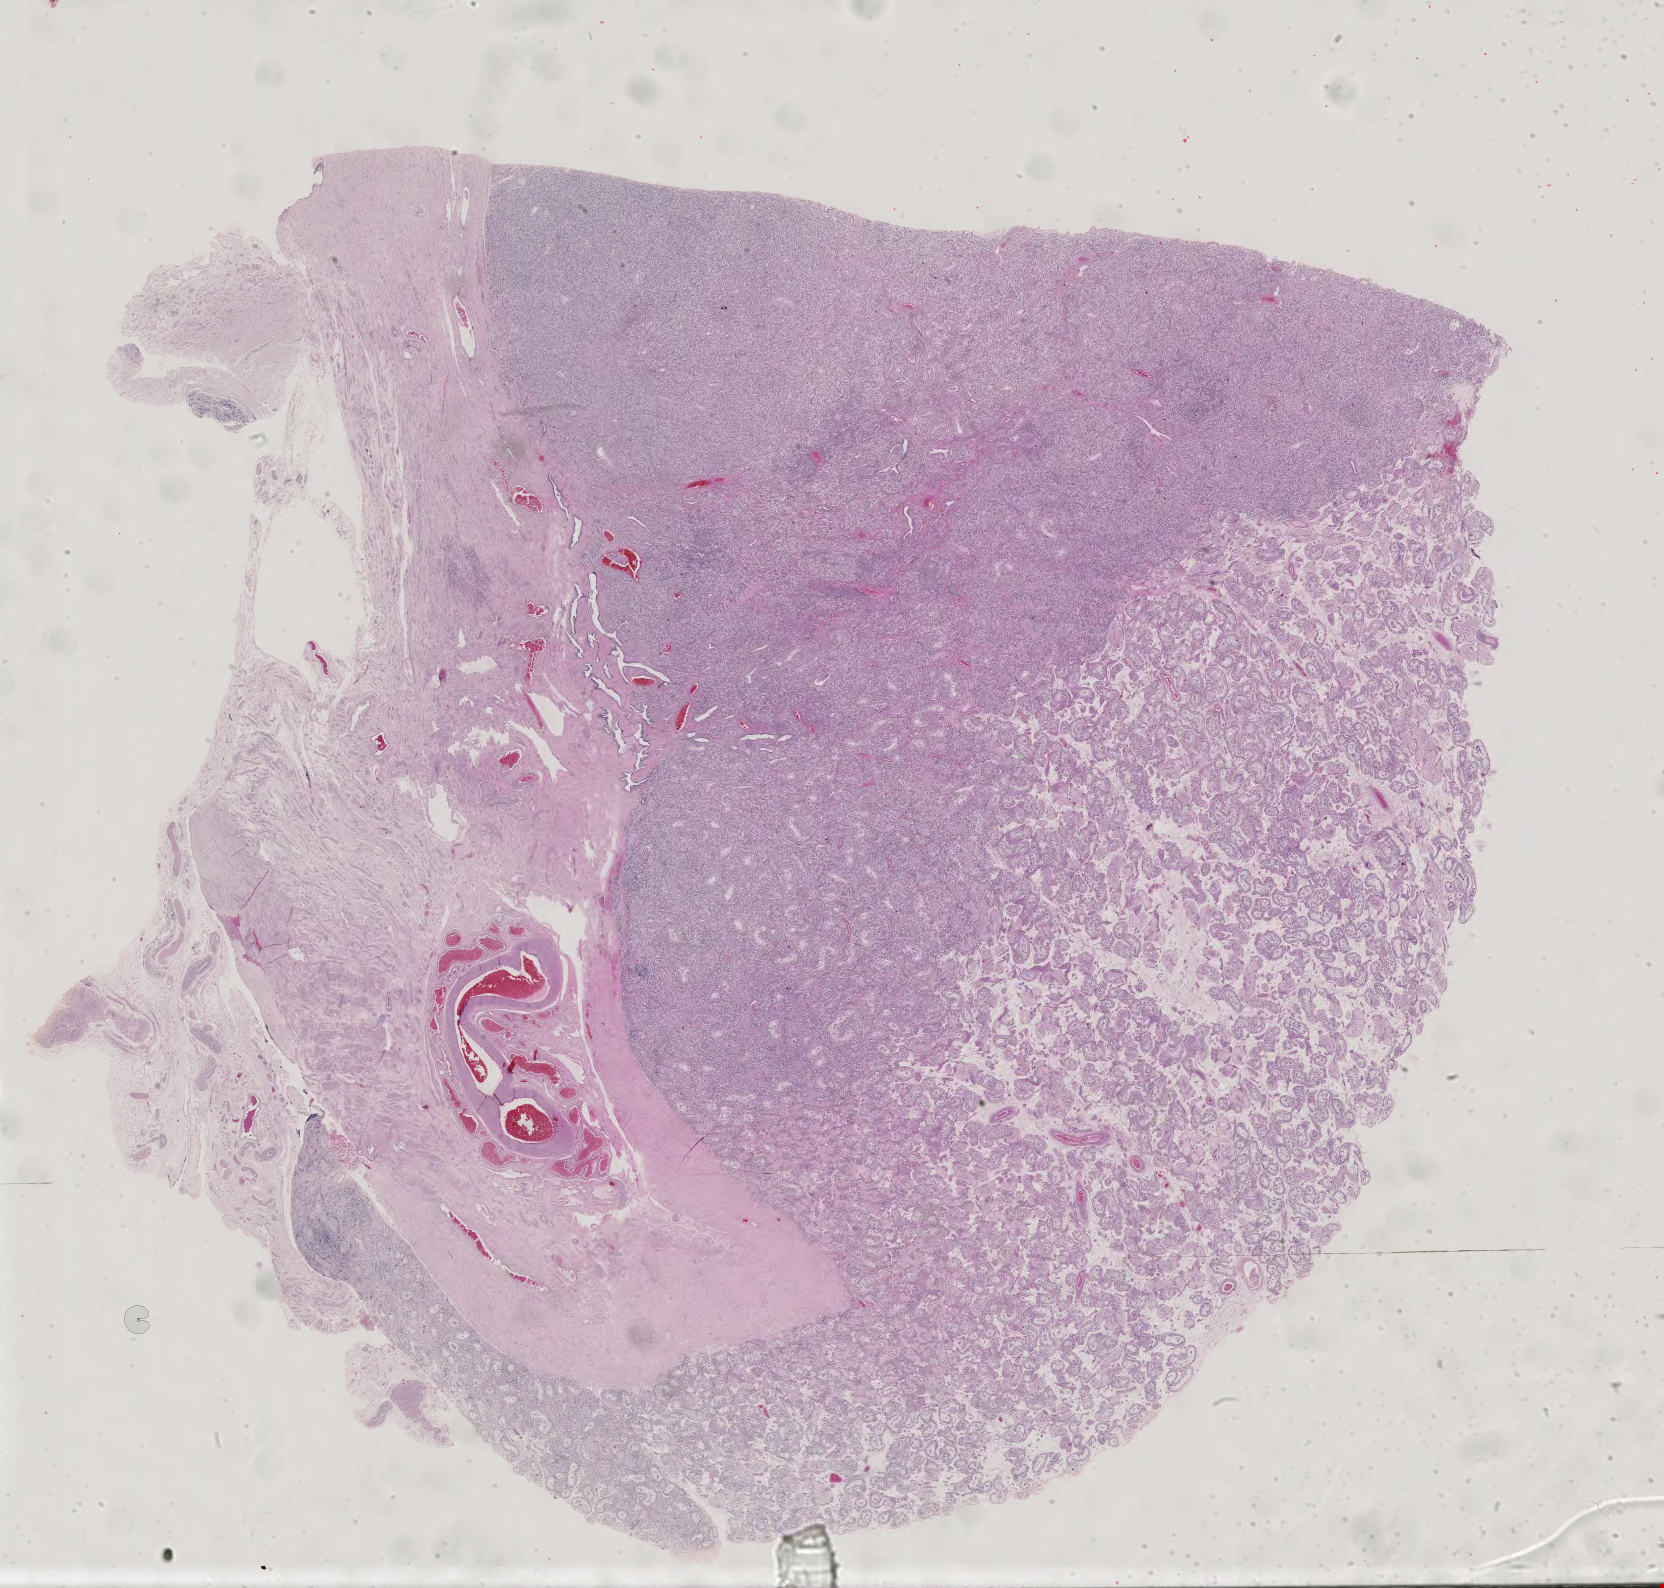
Whole-slide histology image, H&E, shown as a low-resolution overview of the whole scanned area (about 24.2 x 23.1 mm, acquisition: 40x scan), FFPE section, additional new primary tumour sample from the testis. Patient: male, age at initial diagnosis 28 years.
• this section: additional new primary tumour
• patient diagnosis: Teratoma, benign